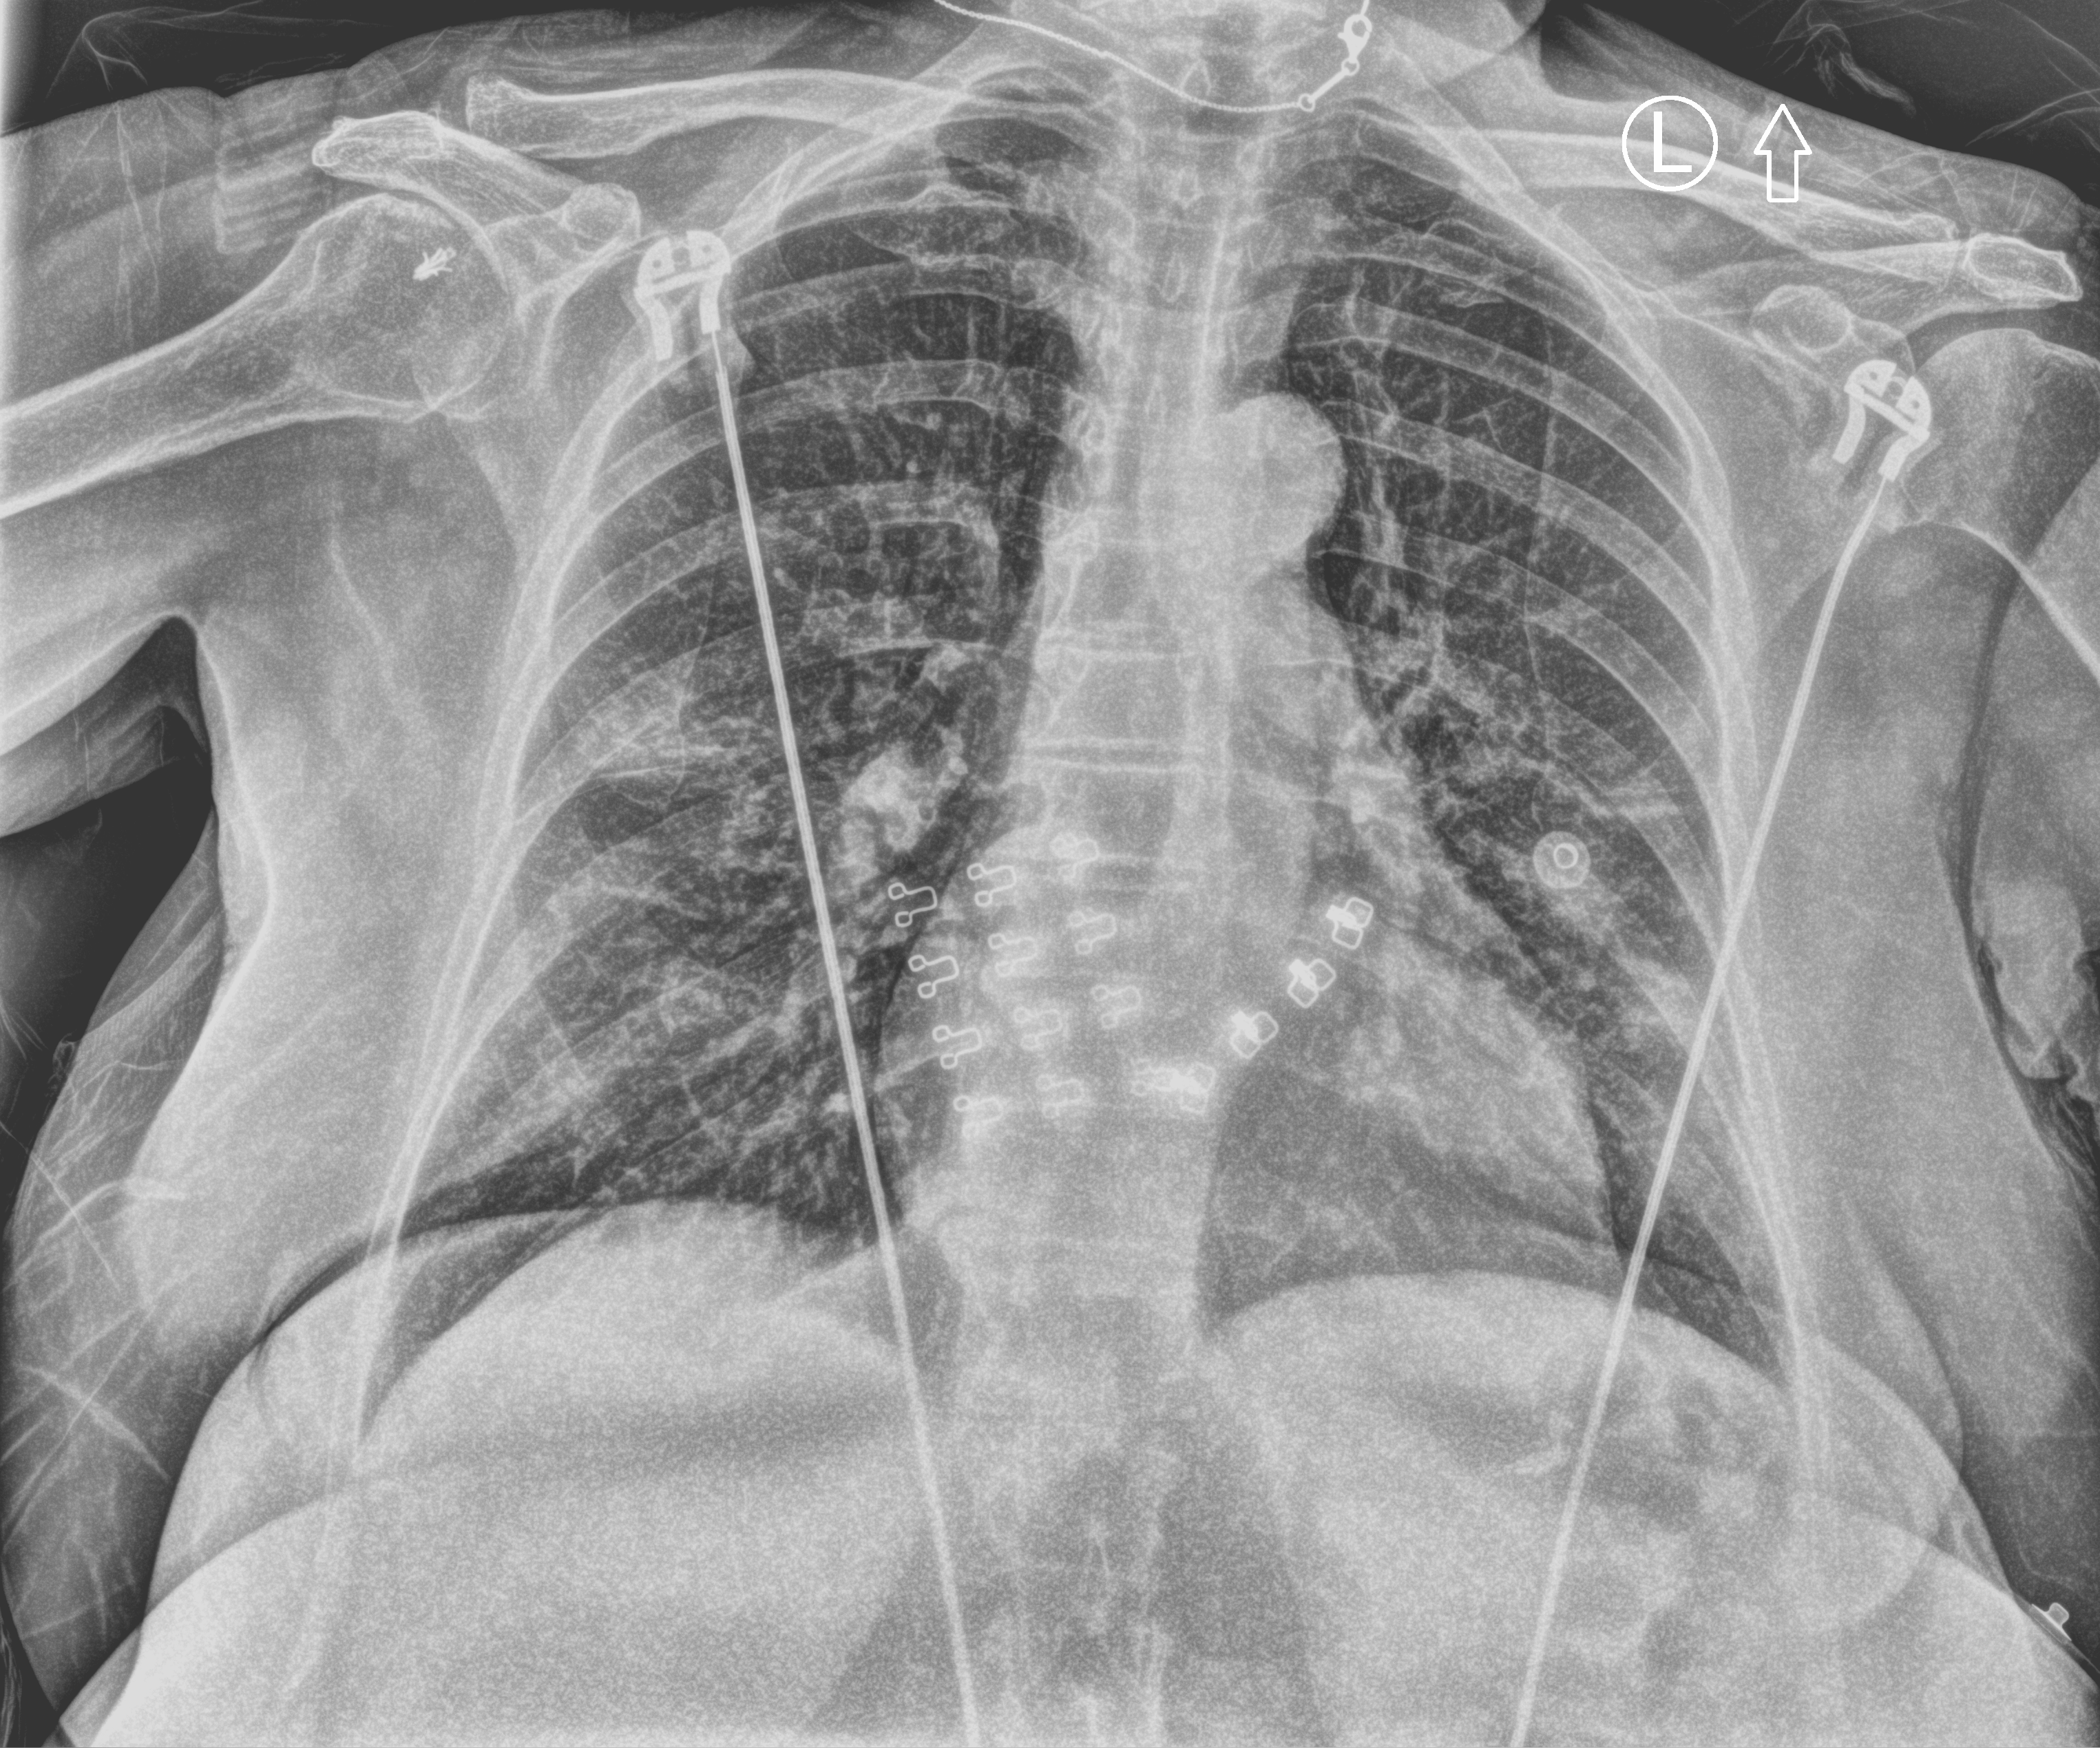
Bedside chest radiograph (computed radiography); anteroposterior (AP) projection. Female patient hospitalised with COVID-19, age 60–74 years.
From the hospital-stay record, not from the radiograph (when in the stay this image was taken is not recorded): length of hospital stay: 8 days; admitted to intensive care during this hospital stay: no.